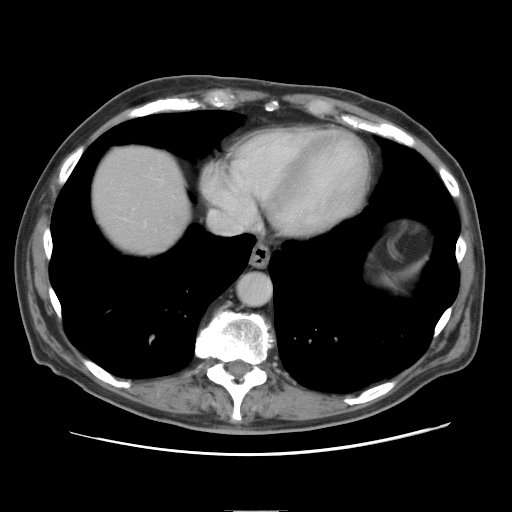
Contrast-enhanced abdominal CT, one axial slice; slice 76 of 89 in the series (ordered by position); 120 kVp; intravenous contrast given; soft-tissue window (W 400 / L 40 HU); 512 × 512 image matrix, field of view 375 × 375 mm. Male patient, age 69 years. From the clinical record (not read from this slice): diagnosis: colorectal cancer liver metastases, imaged before liver resection; multiple liver metastases: no; largest metastasis: 8.5 cm; chemotherapy before resection: no.
Outlined on this slice (manually delineated by an expert):
- liver: bounding box (x1, y1, x2, y2) in pixels: (92, 145, 188, 256)
- planned liver remnant (the part of the liver to remain after resection): (93, 146, 189, 256)